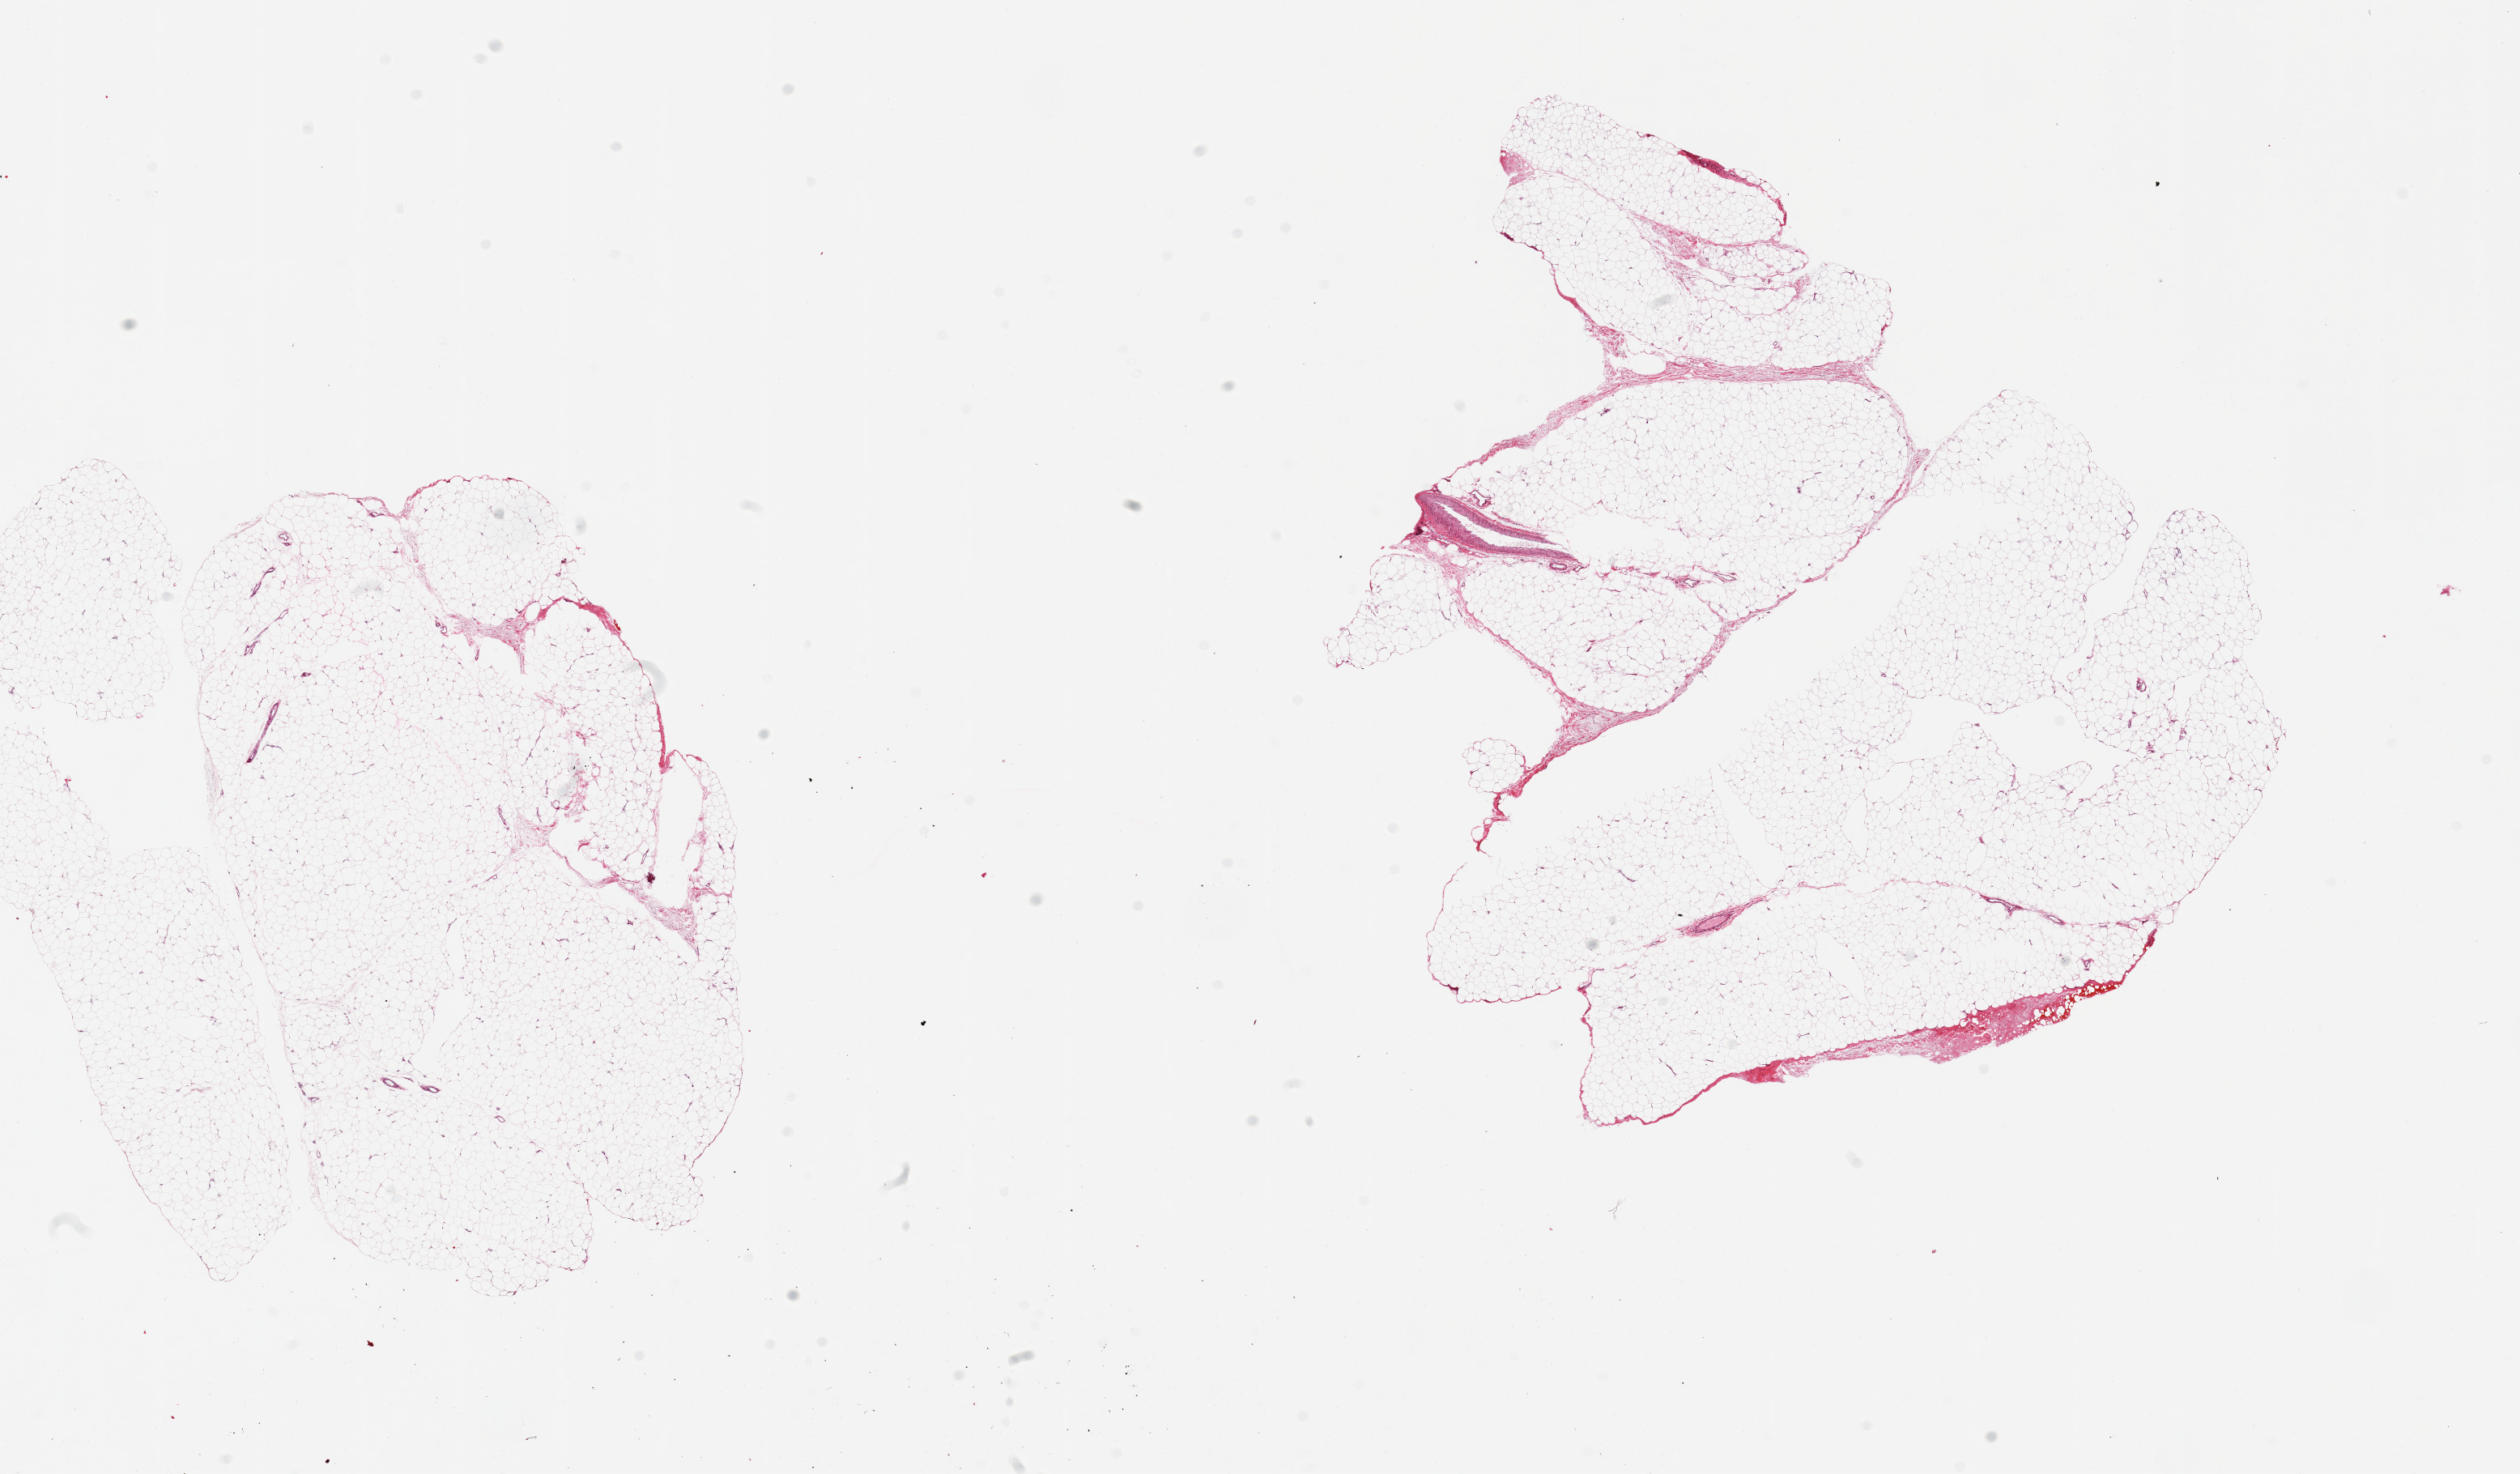
Digitized haematoxylin and eosin-stained section, low-resolution overview of the scanned area, about 24.6 x 14.4 mm (from a 20x scan); PAXgene-fixed paraffin-embedded (PFPE) section; section of adipose tissue (target tissue); donor tissue sample. Donor sex: female.
Reviewer comment on this tissue sample: 2 pieces.